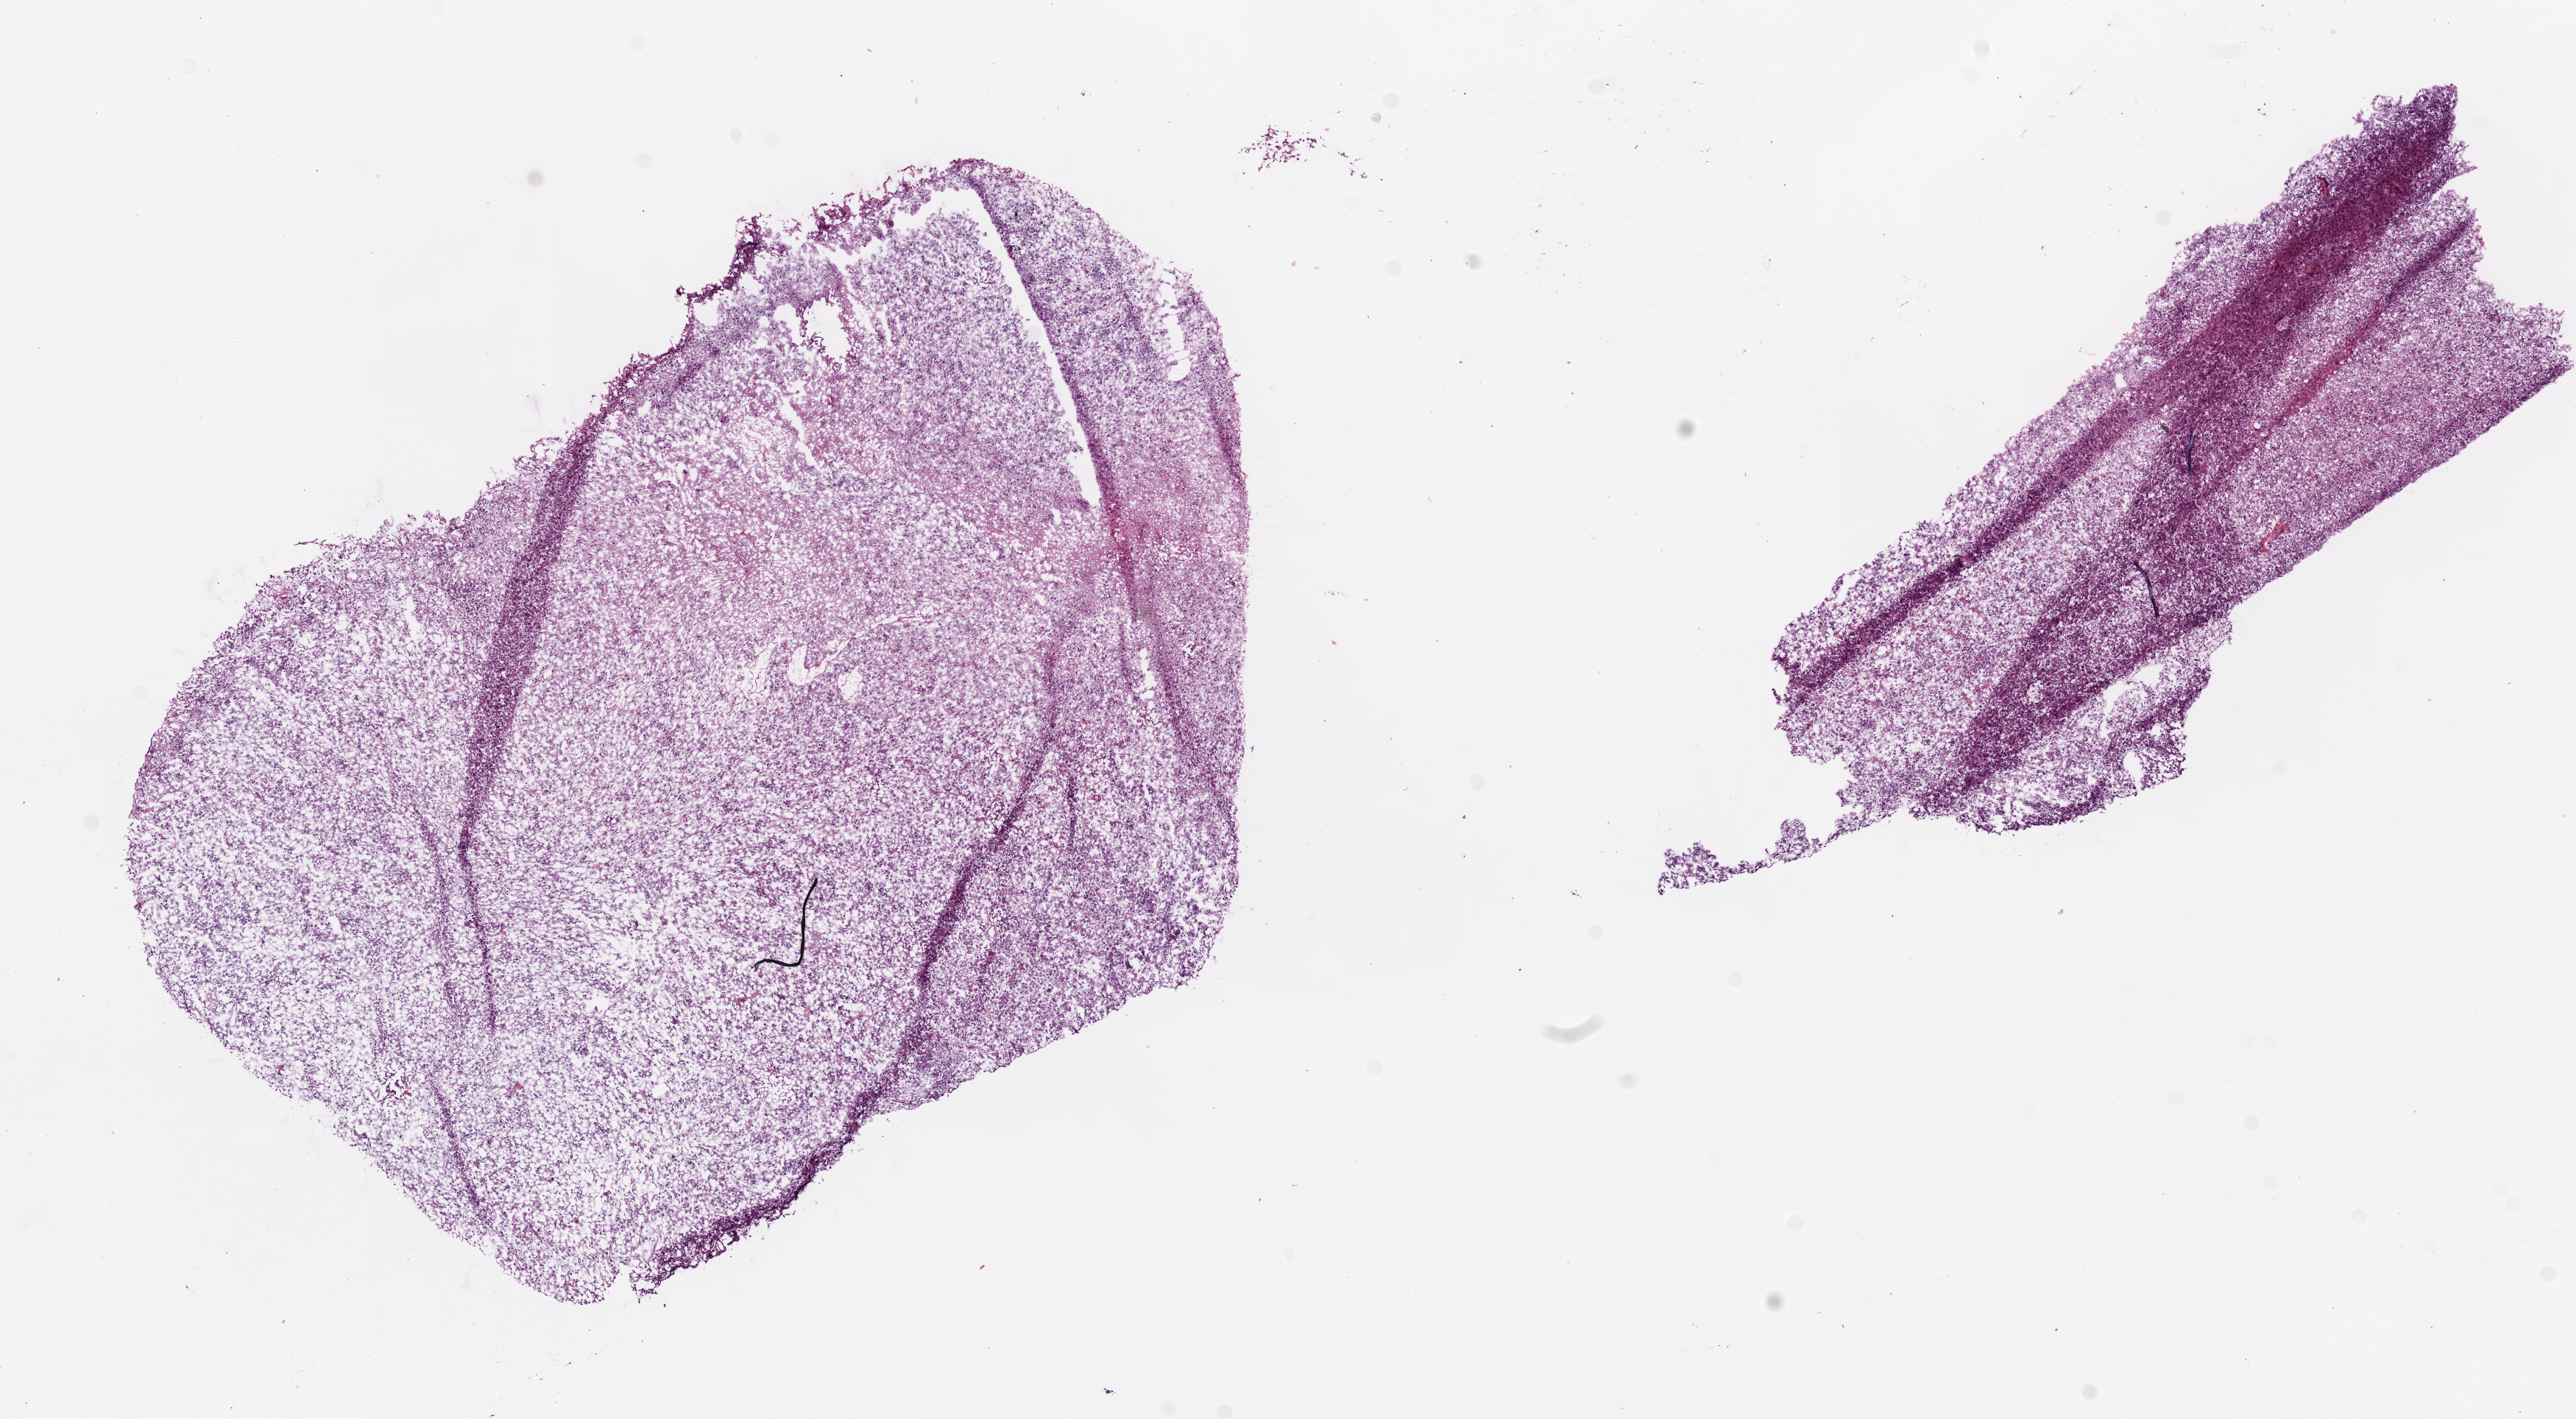
Hematoxylin and eosin (H&E) stained whole-slide image — a low-resolution overview of the entire scanned area, about 14.0 x 7.7 mm (slide scanned at 20x); frozen section from the bottom of the tissue portion; primary tumour sample from the brain. Male, age 67 years at initial diagnosis. Pathologist review of this section (percent, as recorded): tumour cells 99%, tumour nuclei 80%, normal cells 0%, stromal cells 0%, necrosis 1%.
Histologic diagnosis: Glioblastoma.